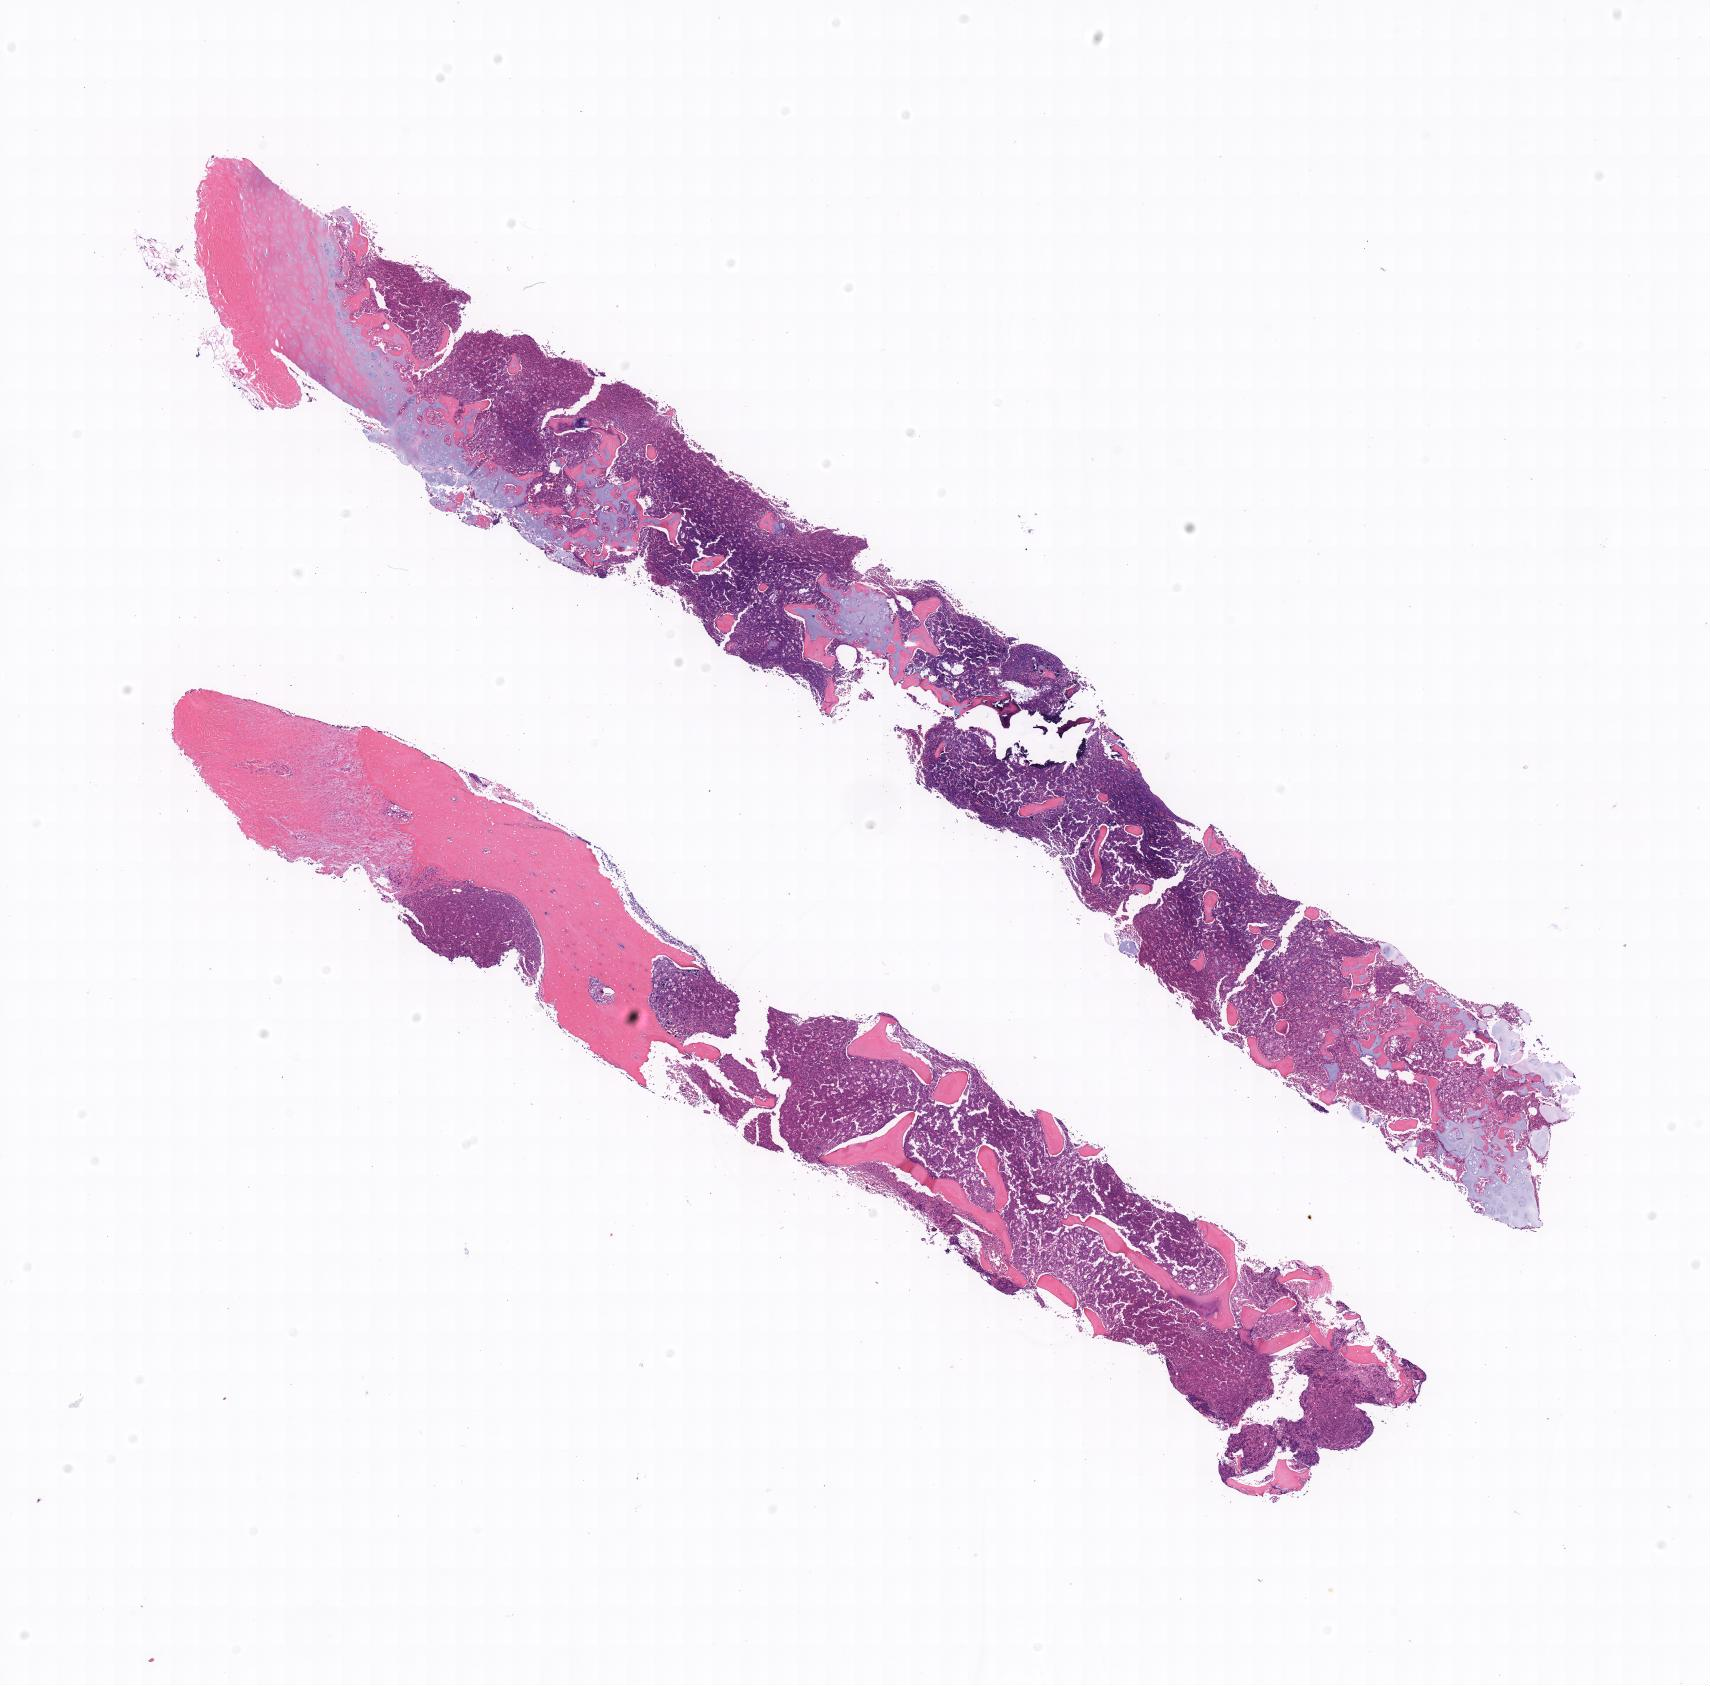
Whole-slide image, H&E stain, shown as a low-resolution overview of the whole scanned area. Tumor tissue. Site: bone marrow. Male patient, 16 years old.
Diagnosis: Burkitt lymphoma, NOS.